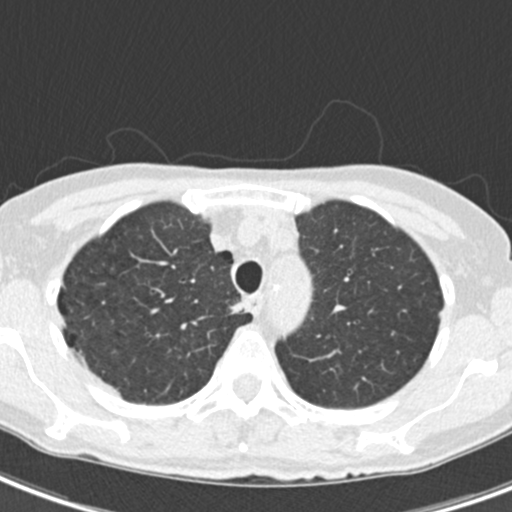
Axial slice from a low-dose chest CT screening exam. Second screening round (one year after baseline). Lung window (W 1500 / L -600 HU). 2 mm slice thickness. Standard (soft-tissue) reconstruction kernel (B30f). Slice 44 of 218 in the series. Female participant, aged 68 years at enrolment. Current smoker at enrolment.
Lesion marked by an expert reader, bounding box <228,300,253,323> (left, top, right, bottom; pixels). Screening reader's record for this exam: no non-calcified nodule ≥4 mm recorded. Official screen result: negative screen, no significant abnormalities.